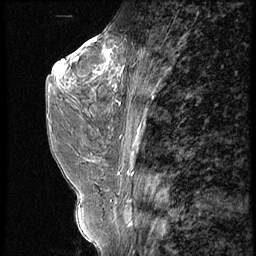
Breast MRI (dynamic contrast-enhanced), one sagittal slice. Position 29 of 56 along the scan axis. 4 images stored at this slice position (order not interpretable as contrast timing). 1.5 T. TE 4.2 ms, TR 9 ms. 2.5 mm slice thickness. 256 × 256 image matrix, field of view 180 × 180 mm. Female patient, age 44 years. Case-level facts recorded for this patient, not image findings: setting: breast cancer imaged before/during neoadjuvant chemotherapy; receptor status: triple-negative.
Outlined on this slice (semi-automatically segmented with operator editing):
- analysis volume of interest (the breast-tissue region the enhancement analysis was run in; not a lesion): box from (x=87, y=28) to (x=132, y=99) px
- tumour enhancement mask (voxels above the 140 % enhancement threshold inside the analysis volume of interest): (x=94, y=48)–(x=123, y=75)